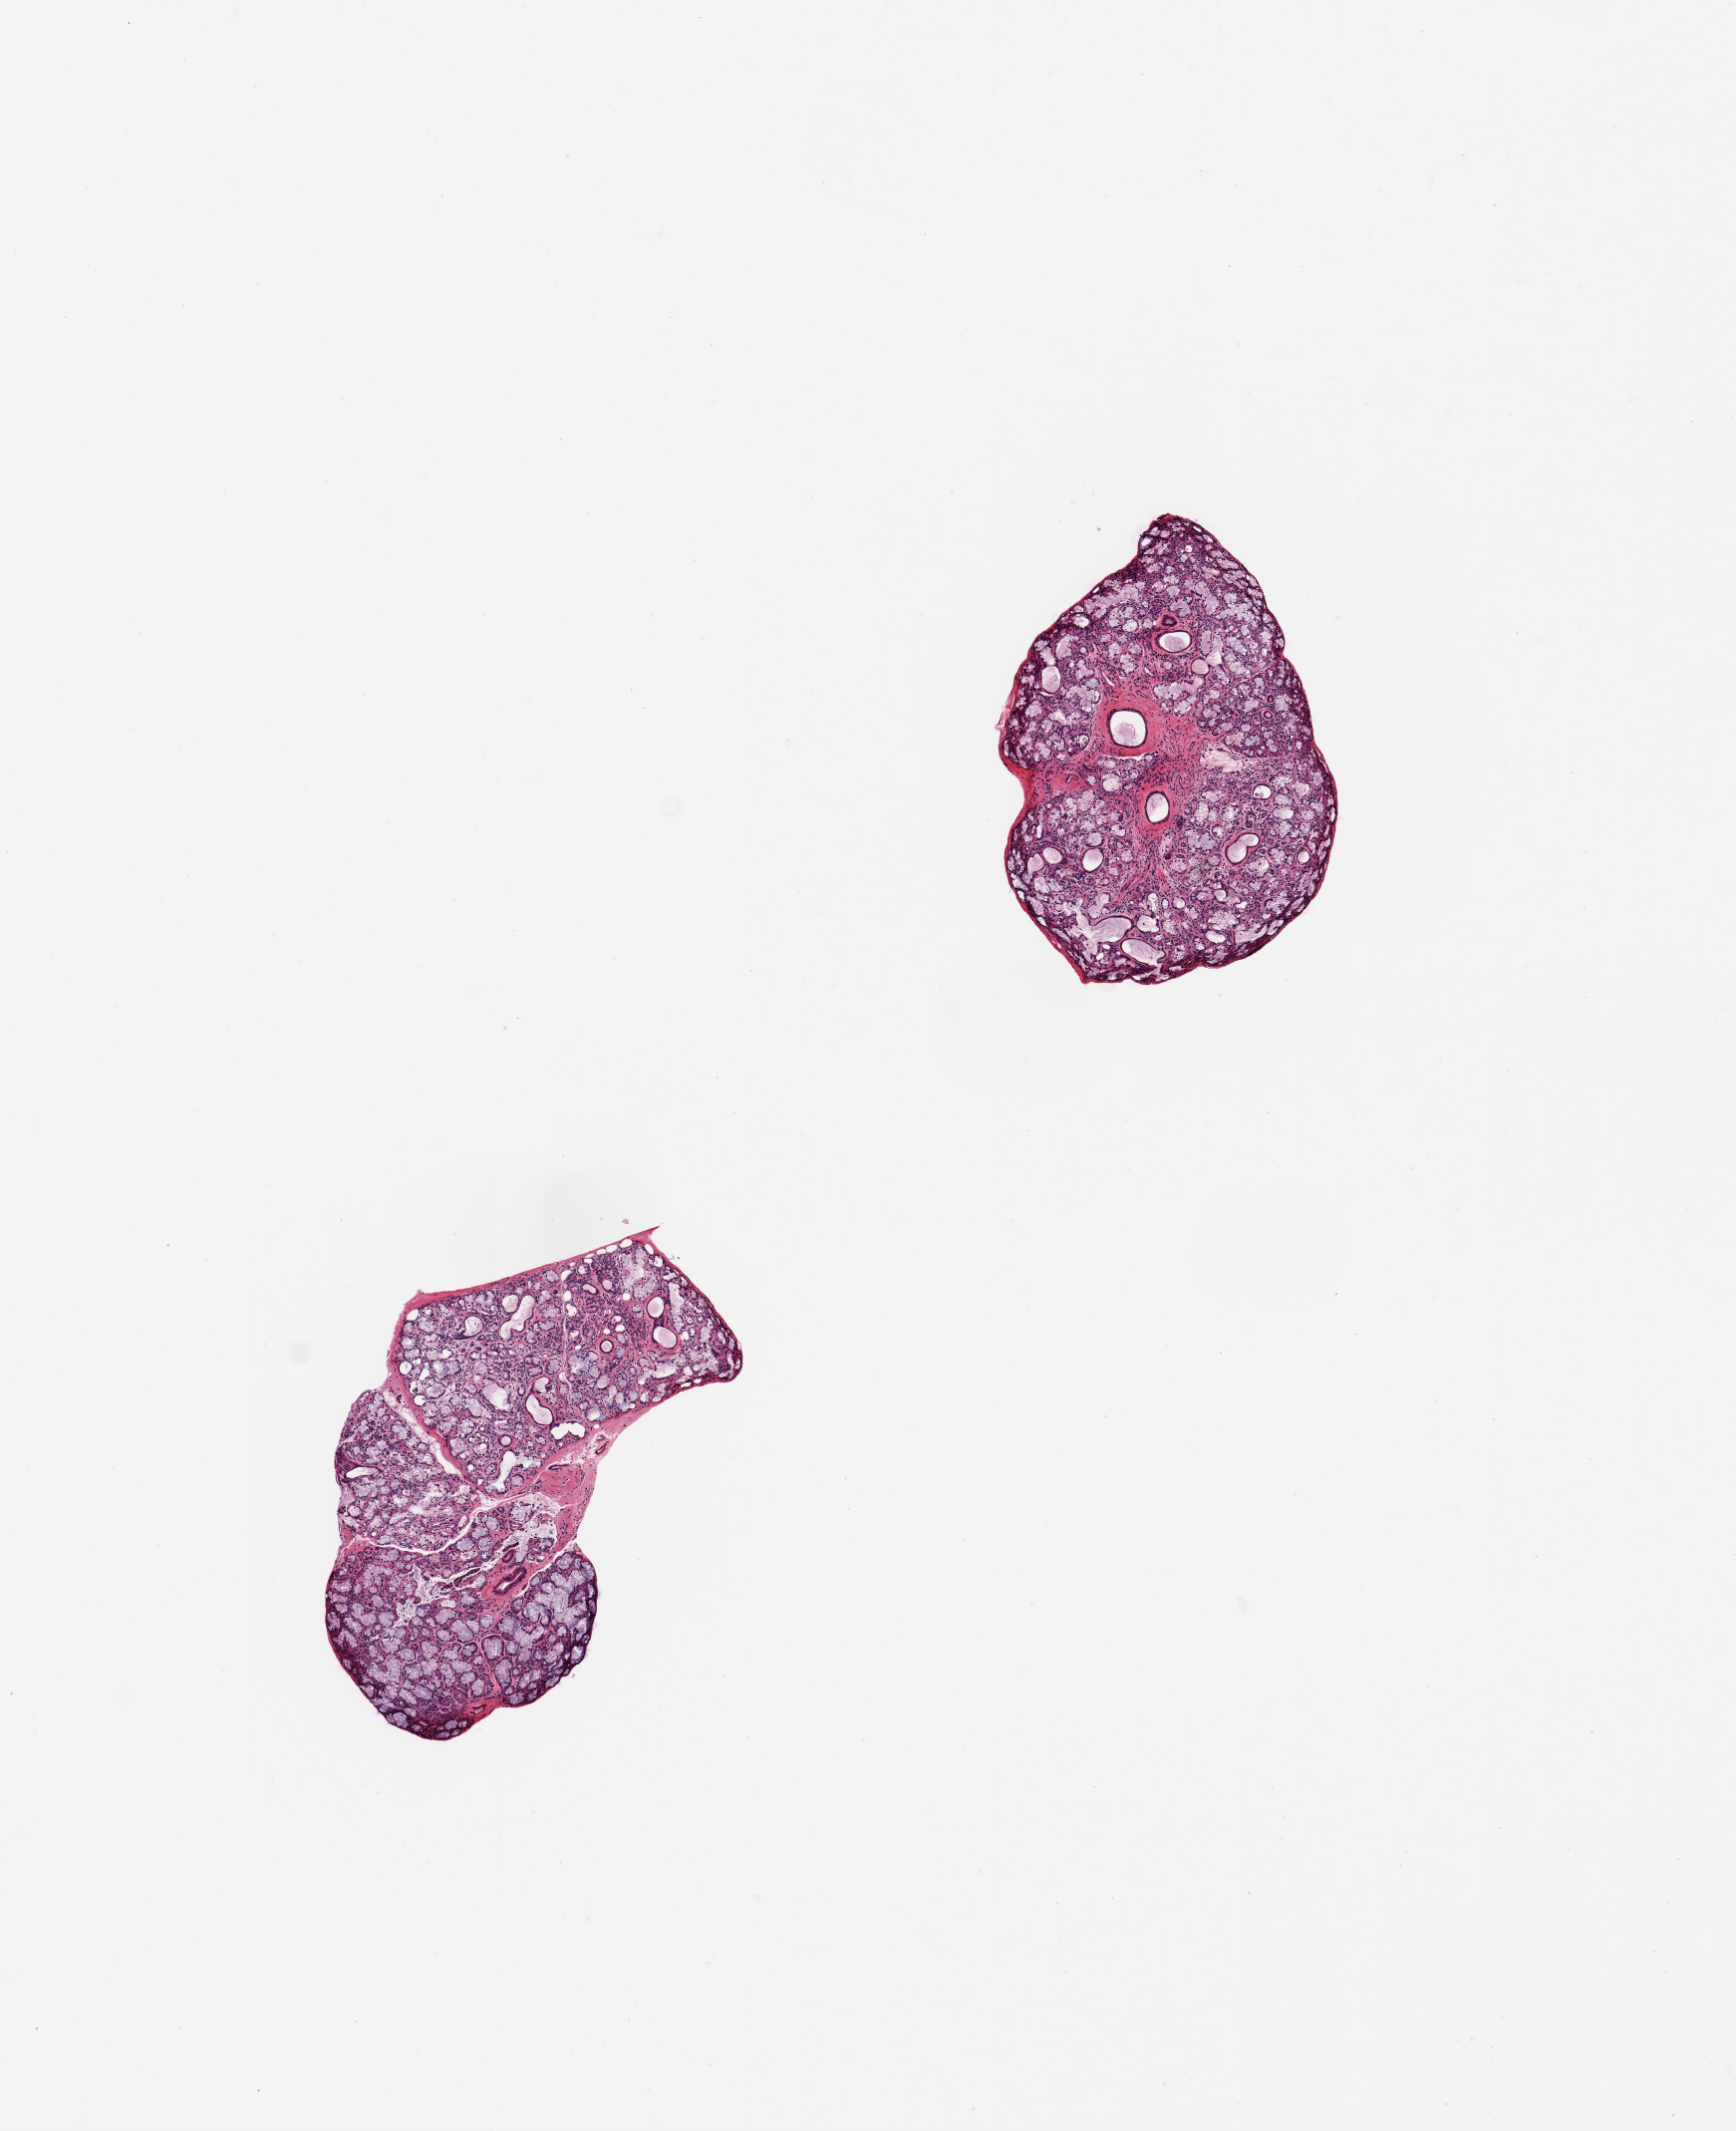
H&E whole-slide image — shown as a low-resolution overview of the whole scanned area (about 6.9 x 8.5 mm); PAXgene-fixed paraffin-embedded (PFPE) section; sampled site (target tissue): minor salivary gland; tissue donor sample. Donor: male.
Reviewer comment on this tissue sample: 2 pieces, all glandular elements.